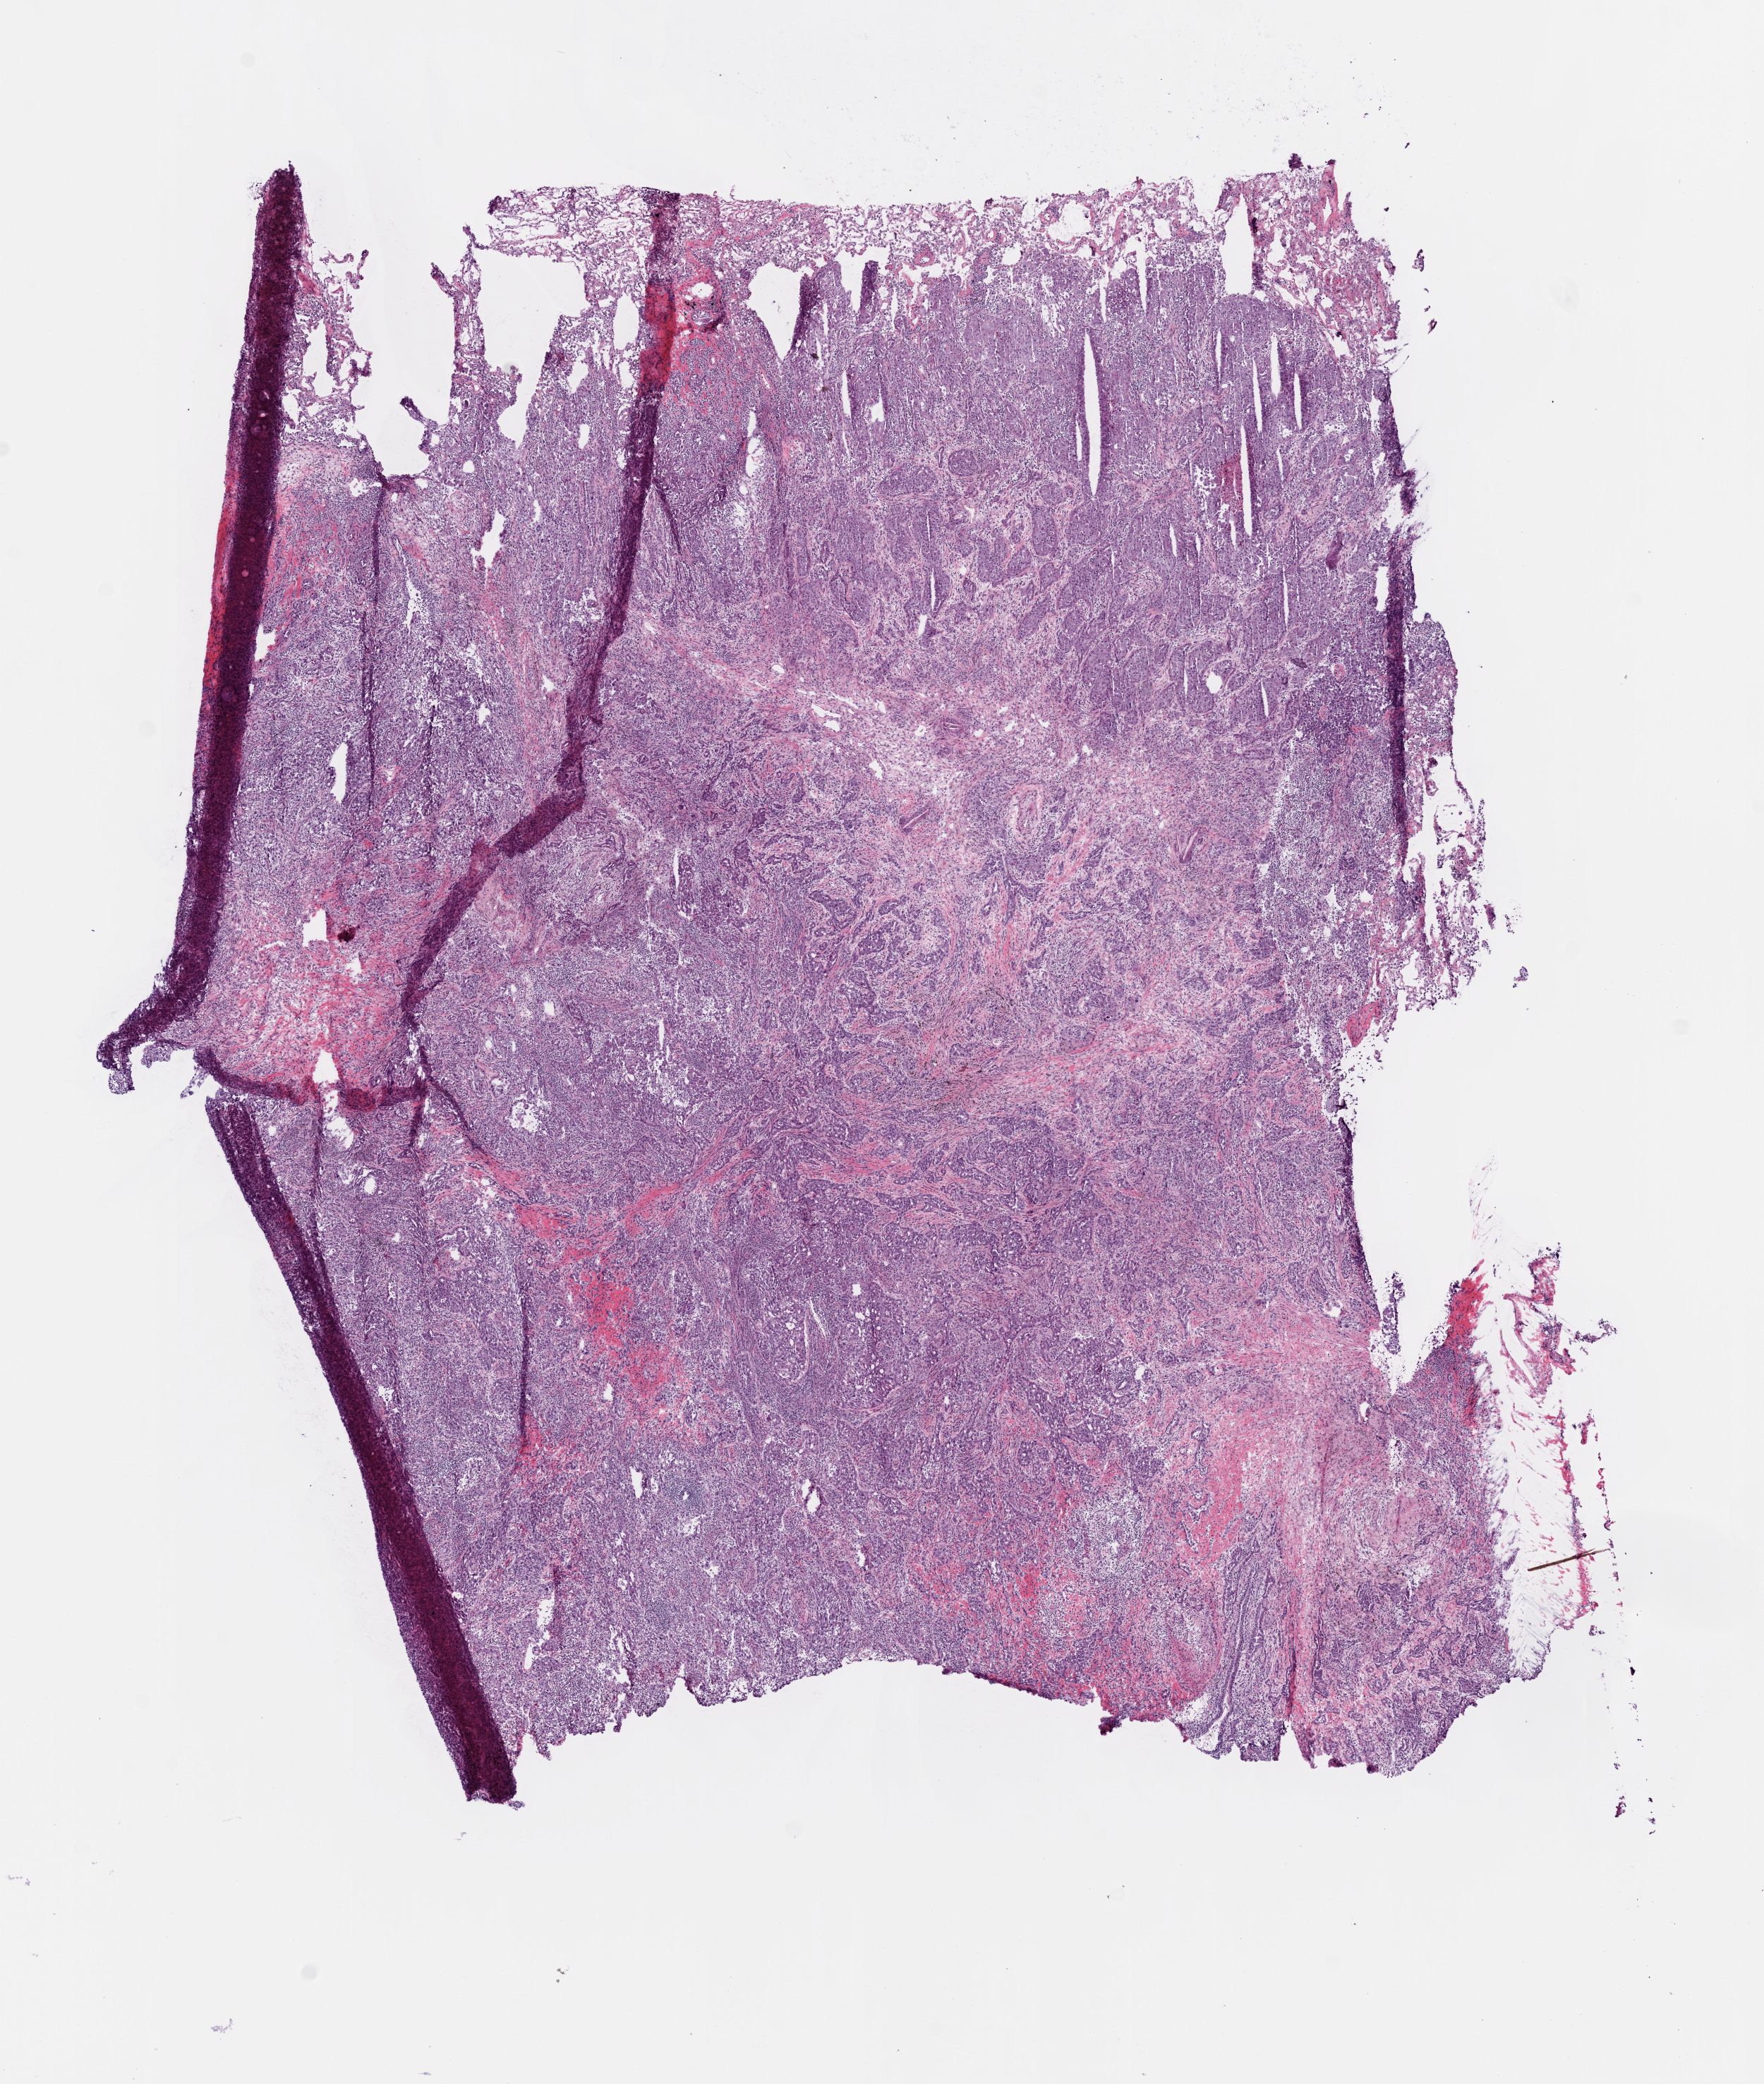
H&E whole-slide image, low-resolution overview of the scanned area, about 10.0 x 11.9 mm; frozen section from the bottom of the tissue portion; lung, primary tumour sample. Patient: male, age at initial diagnosis 59 years. Composition of this section per pathologist review: tumour cells 85%, tumour nuclei 80%, normal cells 3%, stromal cells 12%, necrosis 0%. Infiltration values recorded for this section: lymphocyte infiltration 10%.
Pathologic diagnosis: Adenocarcinoma, NOS (upper lobe, lung). AJCC pathologic stage: IB.